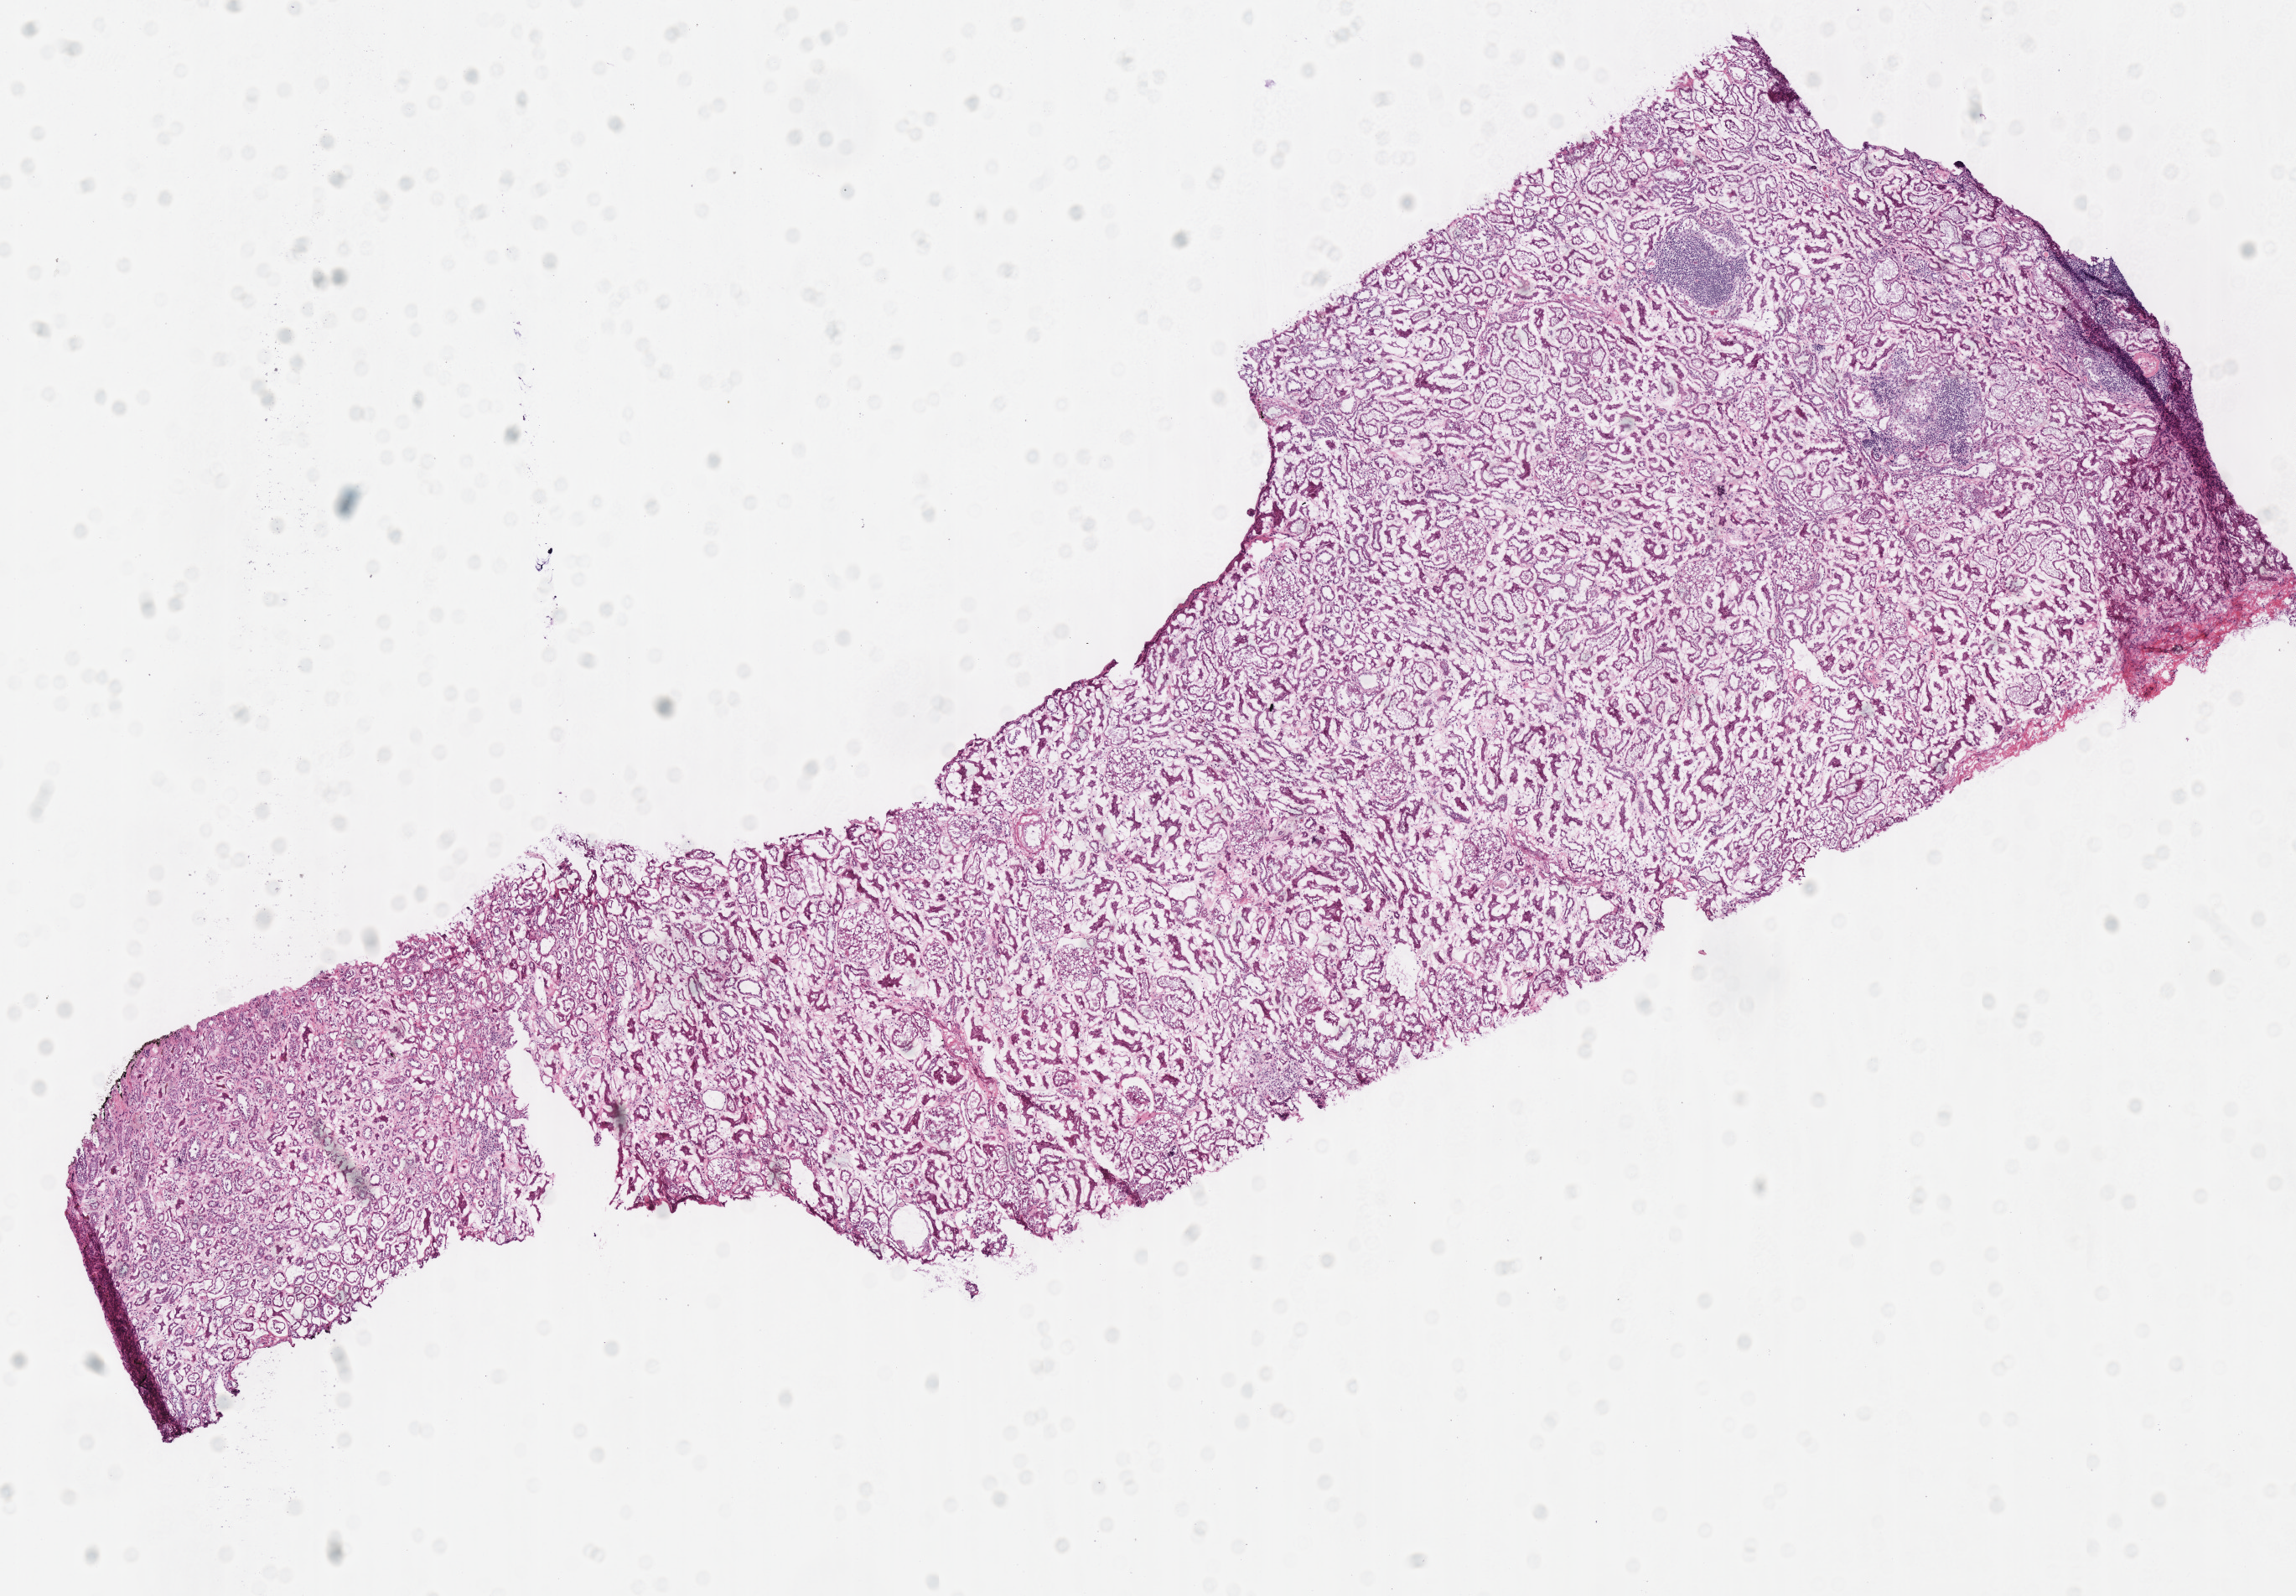
H&E whole-slide image — low-resolution overview of the scanned area, about 10.8 x 7.5 mm. Frozen section. Sample: solid tissue normal (non-tumour tissue), kidney. Male, age 55 years at initial diagnosis.
This section: solid tissue normal sample (biorepository sample class). Patient diagnosis: Papillary adenocarcinoma, NOS.